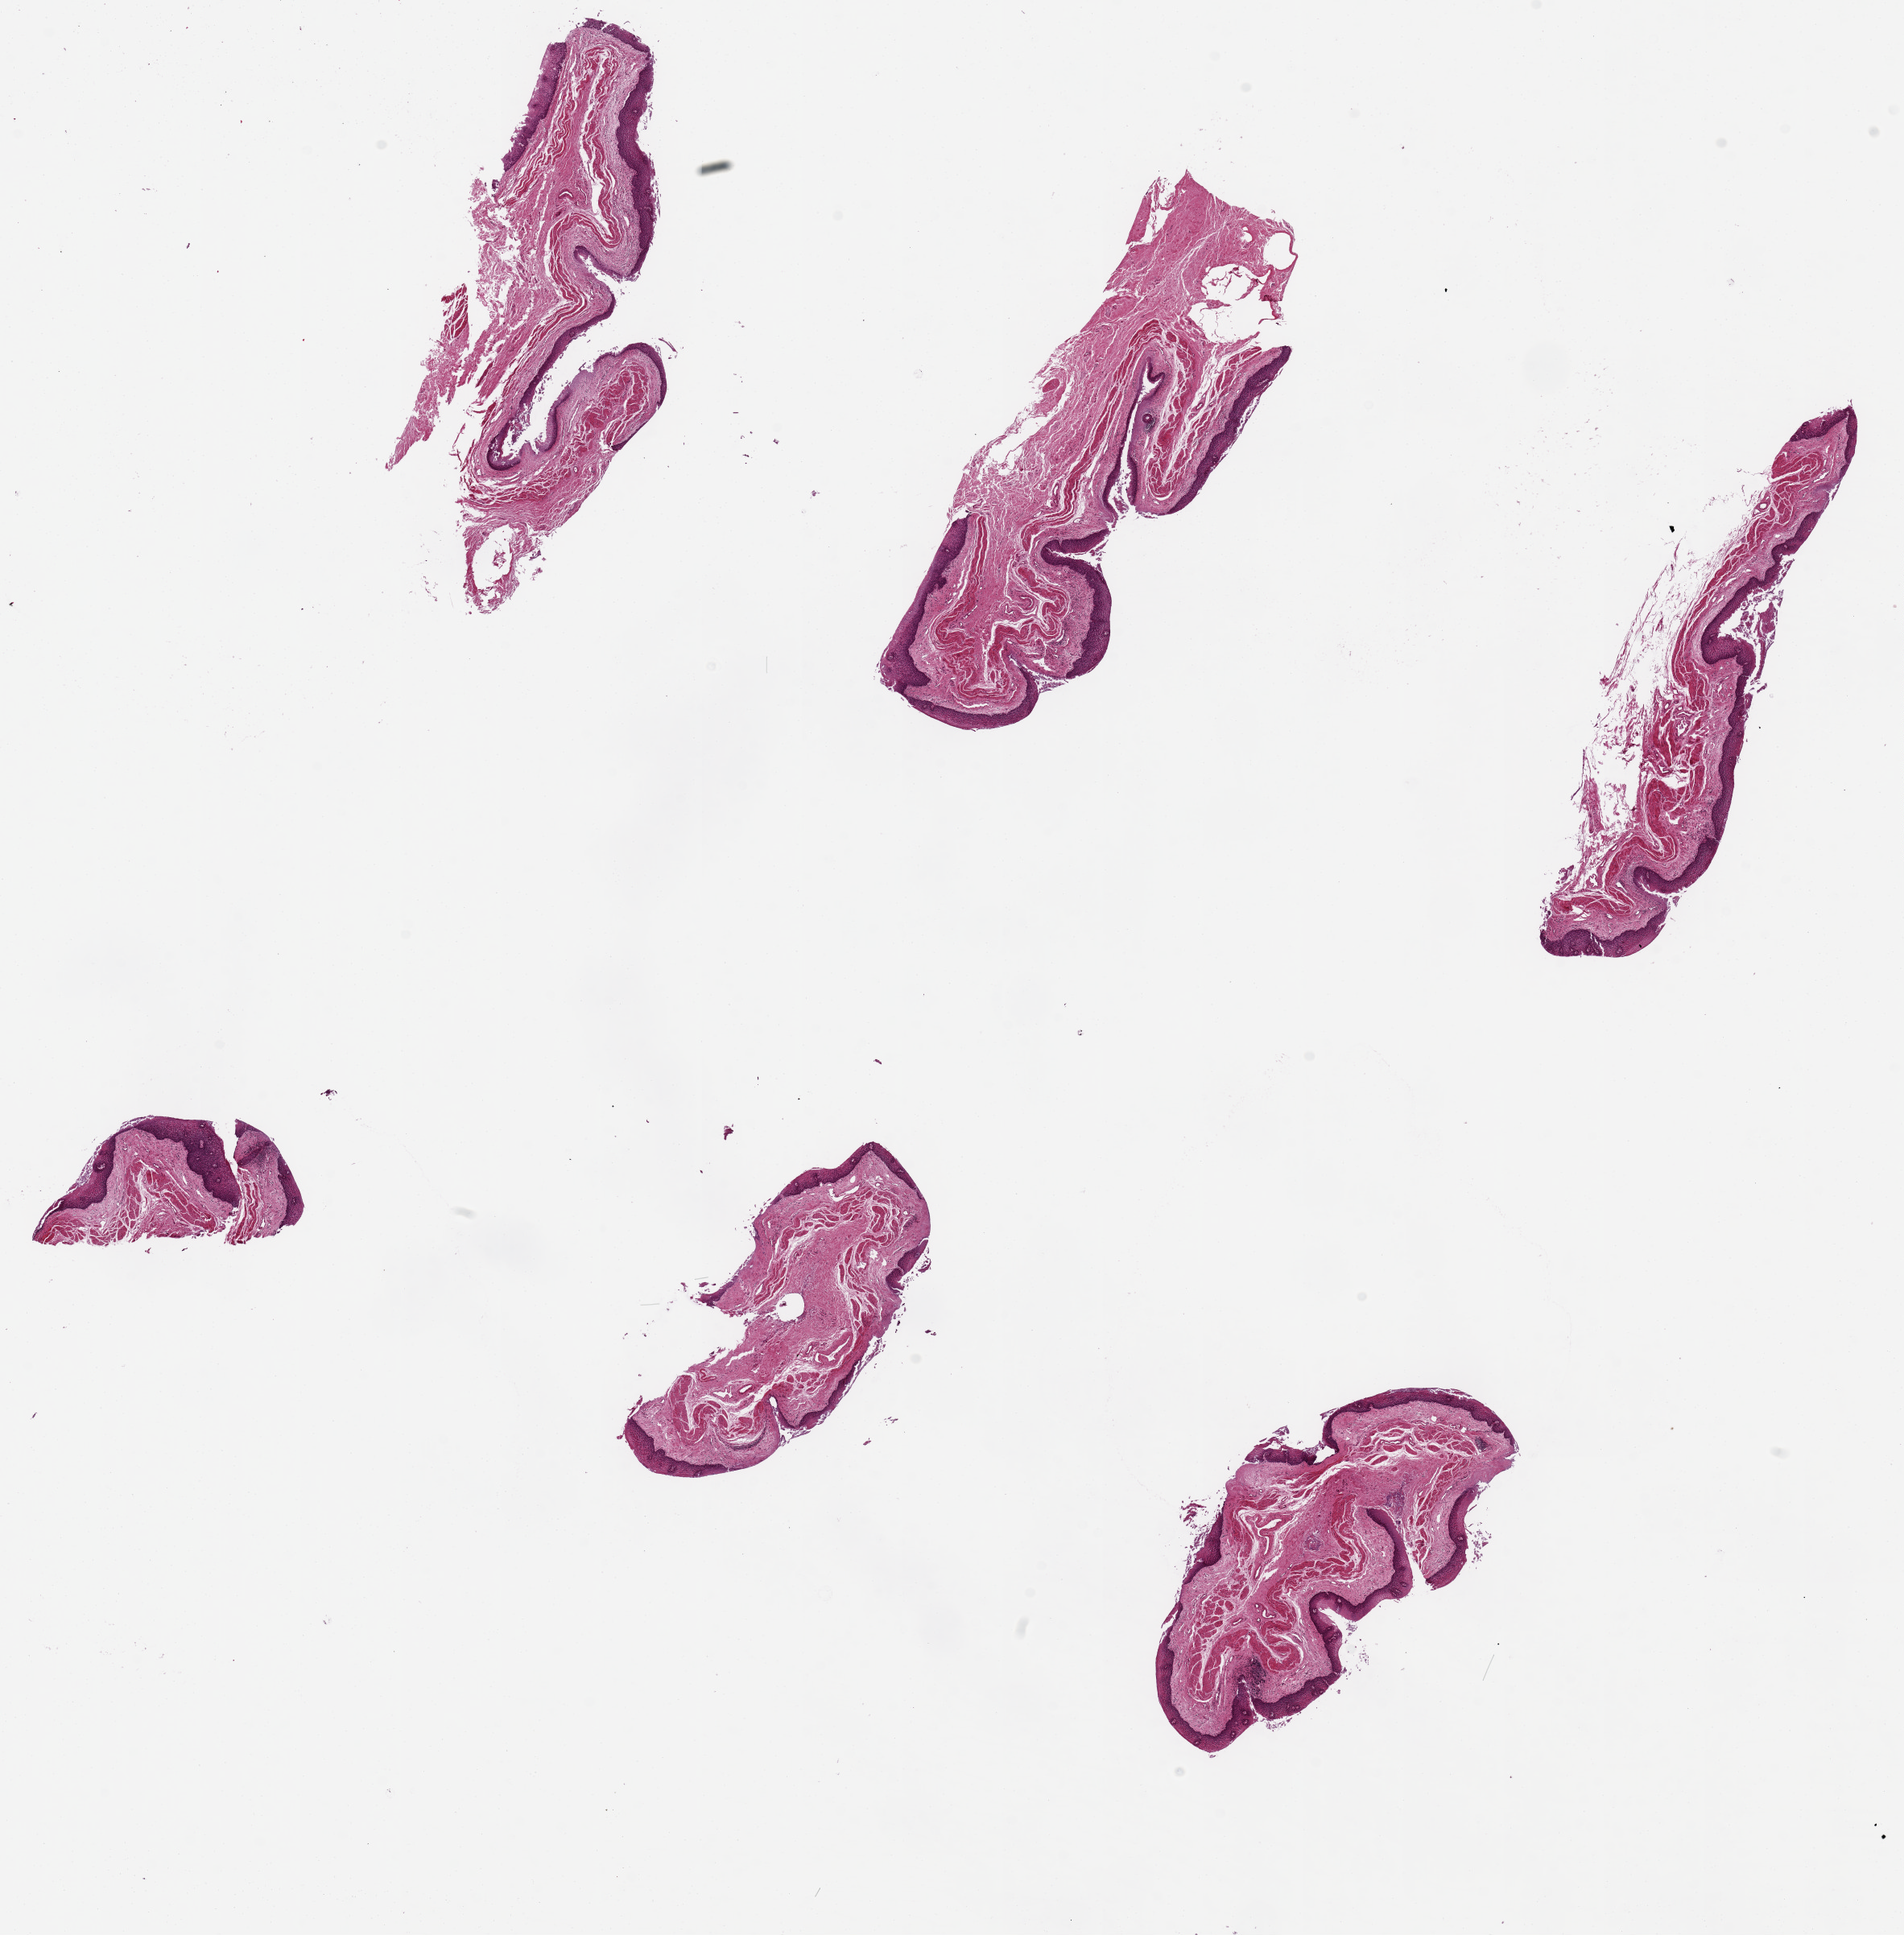
Digitized haematoxylin and eosin-stained section, brightfield, shown as a low-resolution overview of the whole scanned area (about 18.7 x 19.0 mm, slide scanned at 20x). PAXgene-fixed paraffin-embedded (PFPE) section. Section of esophageal mucous membrane (target tissue). Tissue donor sample.
- reviewer comment on this tissue sample: 6 pieces ~6x1.5mm. Squamous mucosa is ~10-15% of thickness